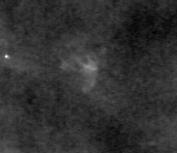
Cropped region of a digitized screen-film mammogram centred on a radiologist-marked abnormality; right breast; CC view.
- Marked abnormality: calcifications, morphology pleomorphic, distribution clustered; BI-RADS assessment category 4; subtlety rating 2 on a 1 (subtle) to 5 (obvious) scale; pathology result (as recorded, not read from the image): benign.